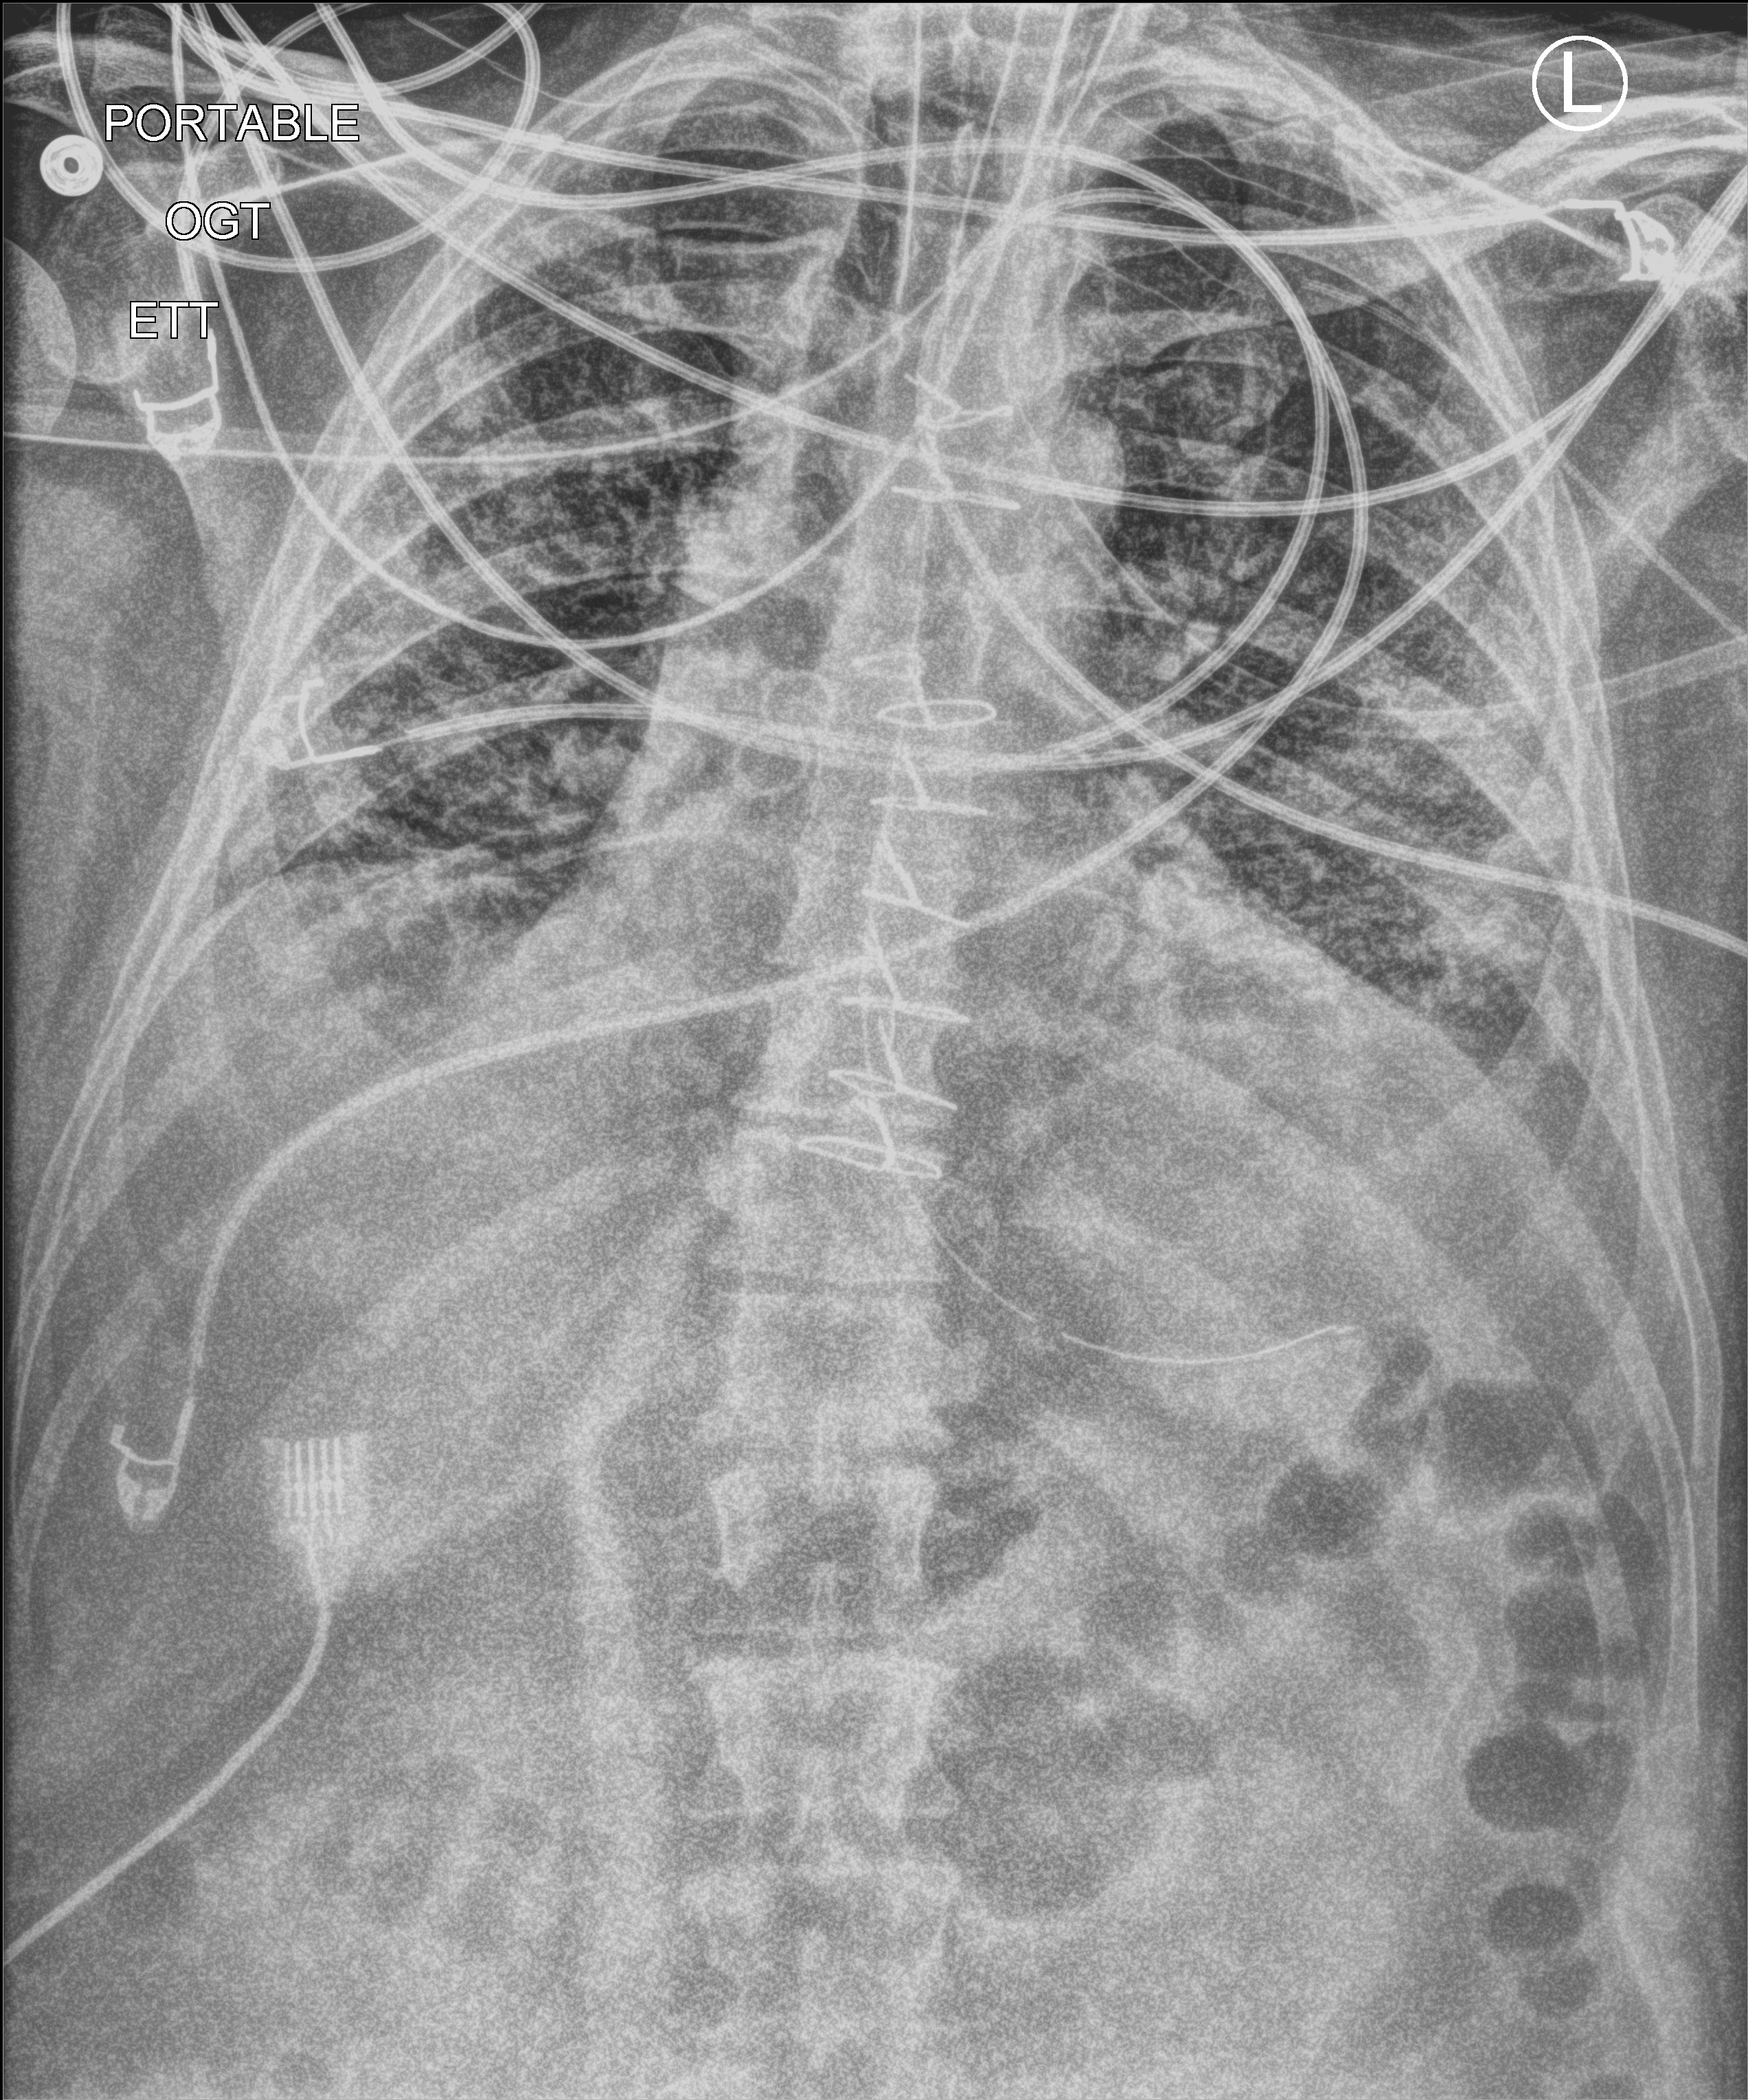
Bedside chest radiograph (computed radiography), anteroposterior (AP) projection. Patient hospitalised with COVID-19; male, aged 18–59 years.
Hospital-stay facts (about this admission, not read from this image; timing relative to this image not recorded):
- admitted to intensive care during this hospital stay: yes
- other chronic lung disease (admission record): yes